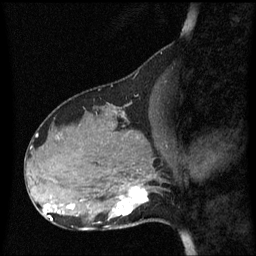
Breast MRI (dynamic contrast-enhanced), one sagittal slice; slice 24 of 60 in the series (ordered by position); dynamic contrast-enhanced series, image 2 of 3 at this slice position (ordered by acquisition); 1.5 T; TE 4.2 ms, TR 8.4 ms; 256 × 256 image matrix. Patient: female, 31 years. Case-level facts recorded for this patient, not image findings: setting: breast cancer imaged before/during neoadjuvant chemotherapy; receptor status: HR-positive, HER2-negative.
Outlined on this slice (semi-automatic segmentation, software-assisted and operator-edited):
- analysis volume of interest (the breast-tissue region the enhancement analysis was run in; not a lesion): bounding box <98,175,162,228> (left, top, right, bottom; pixels)
- tumour enhancement mask (voxels above the 70 % enhancement threshold inside the analysis volume of interest): <100,187,149,224>